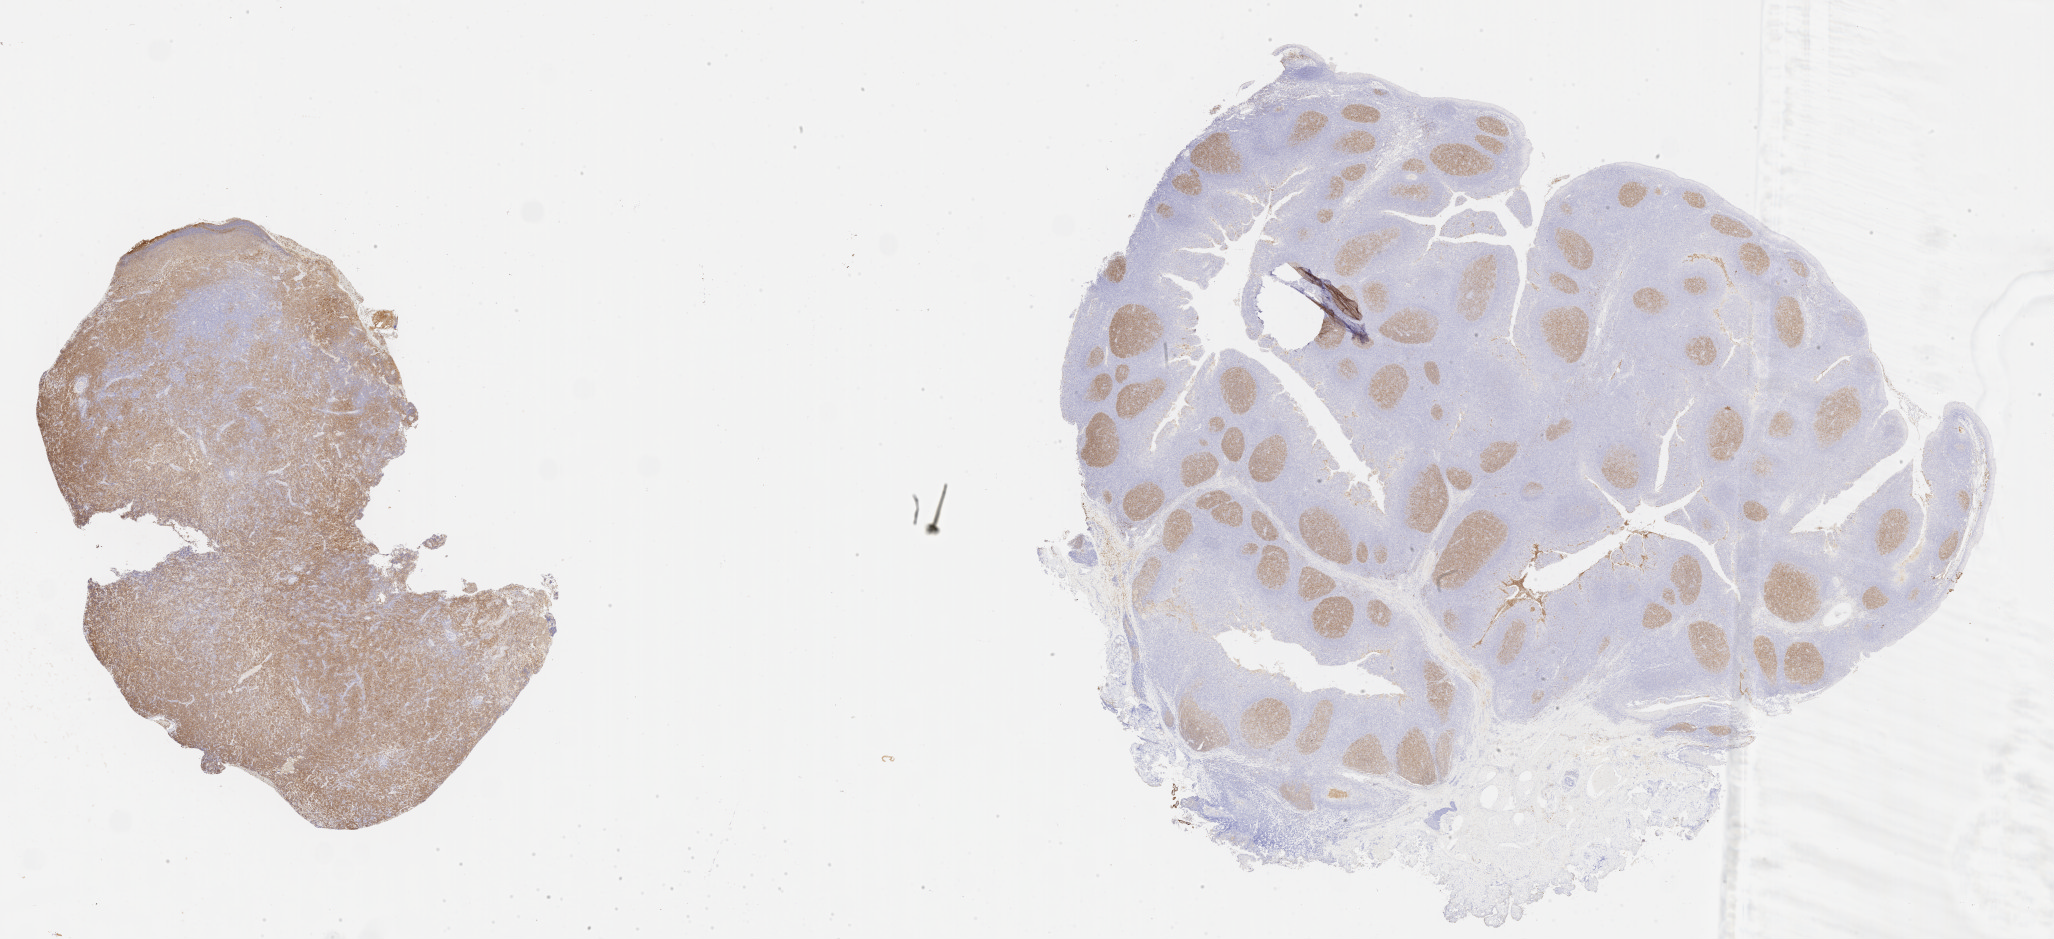
Whole-slide image, immunohistochemical stain for CD10, whole scanned area (about 33.2 x 15.2 mm) shown as a low-resolution overview, tumor tissue. Male, age 7 years at initial diagnosis.
* diagnosis: Diffuse large B-cell lymphoma, NOS